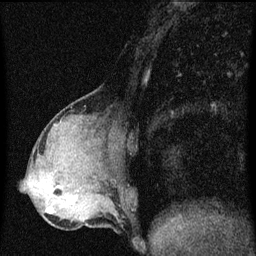
Breast MRI (dynamic contrast-enhanced), one sagittal slice; position 25 of 60 along the scan axis; dynamic contrast-enhanced series, image 2 of 3 at this slice position (ordered by acquisition); 1.5 T; TE 4.2 ms, TR 8 ms; 2 mm slice thickness; 256 × 256 image matrix. Female patient, age 49 years.
Annotated regions visible in this slice (semi-automatically segmented with operator editing):
- analysis volume of interest (the breast-tissue region the enhancement analysis was run in; not a lesion): bounding box [x1, y1, x2, y2] px = [43, 190, 88, 219]
- tumour enhancement mask (voxels above the 70 % enhancement threshold inside the analysis volume of interest): [46, 196, 74, 213]